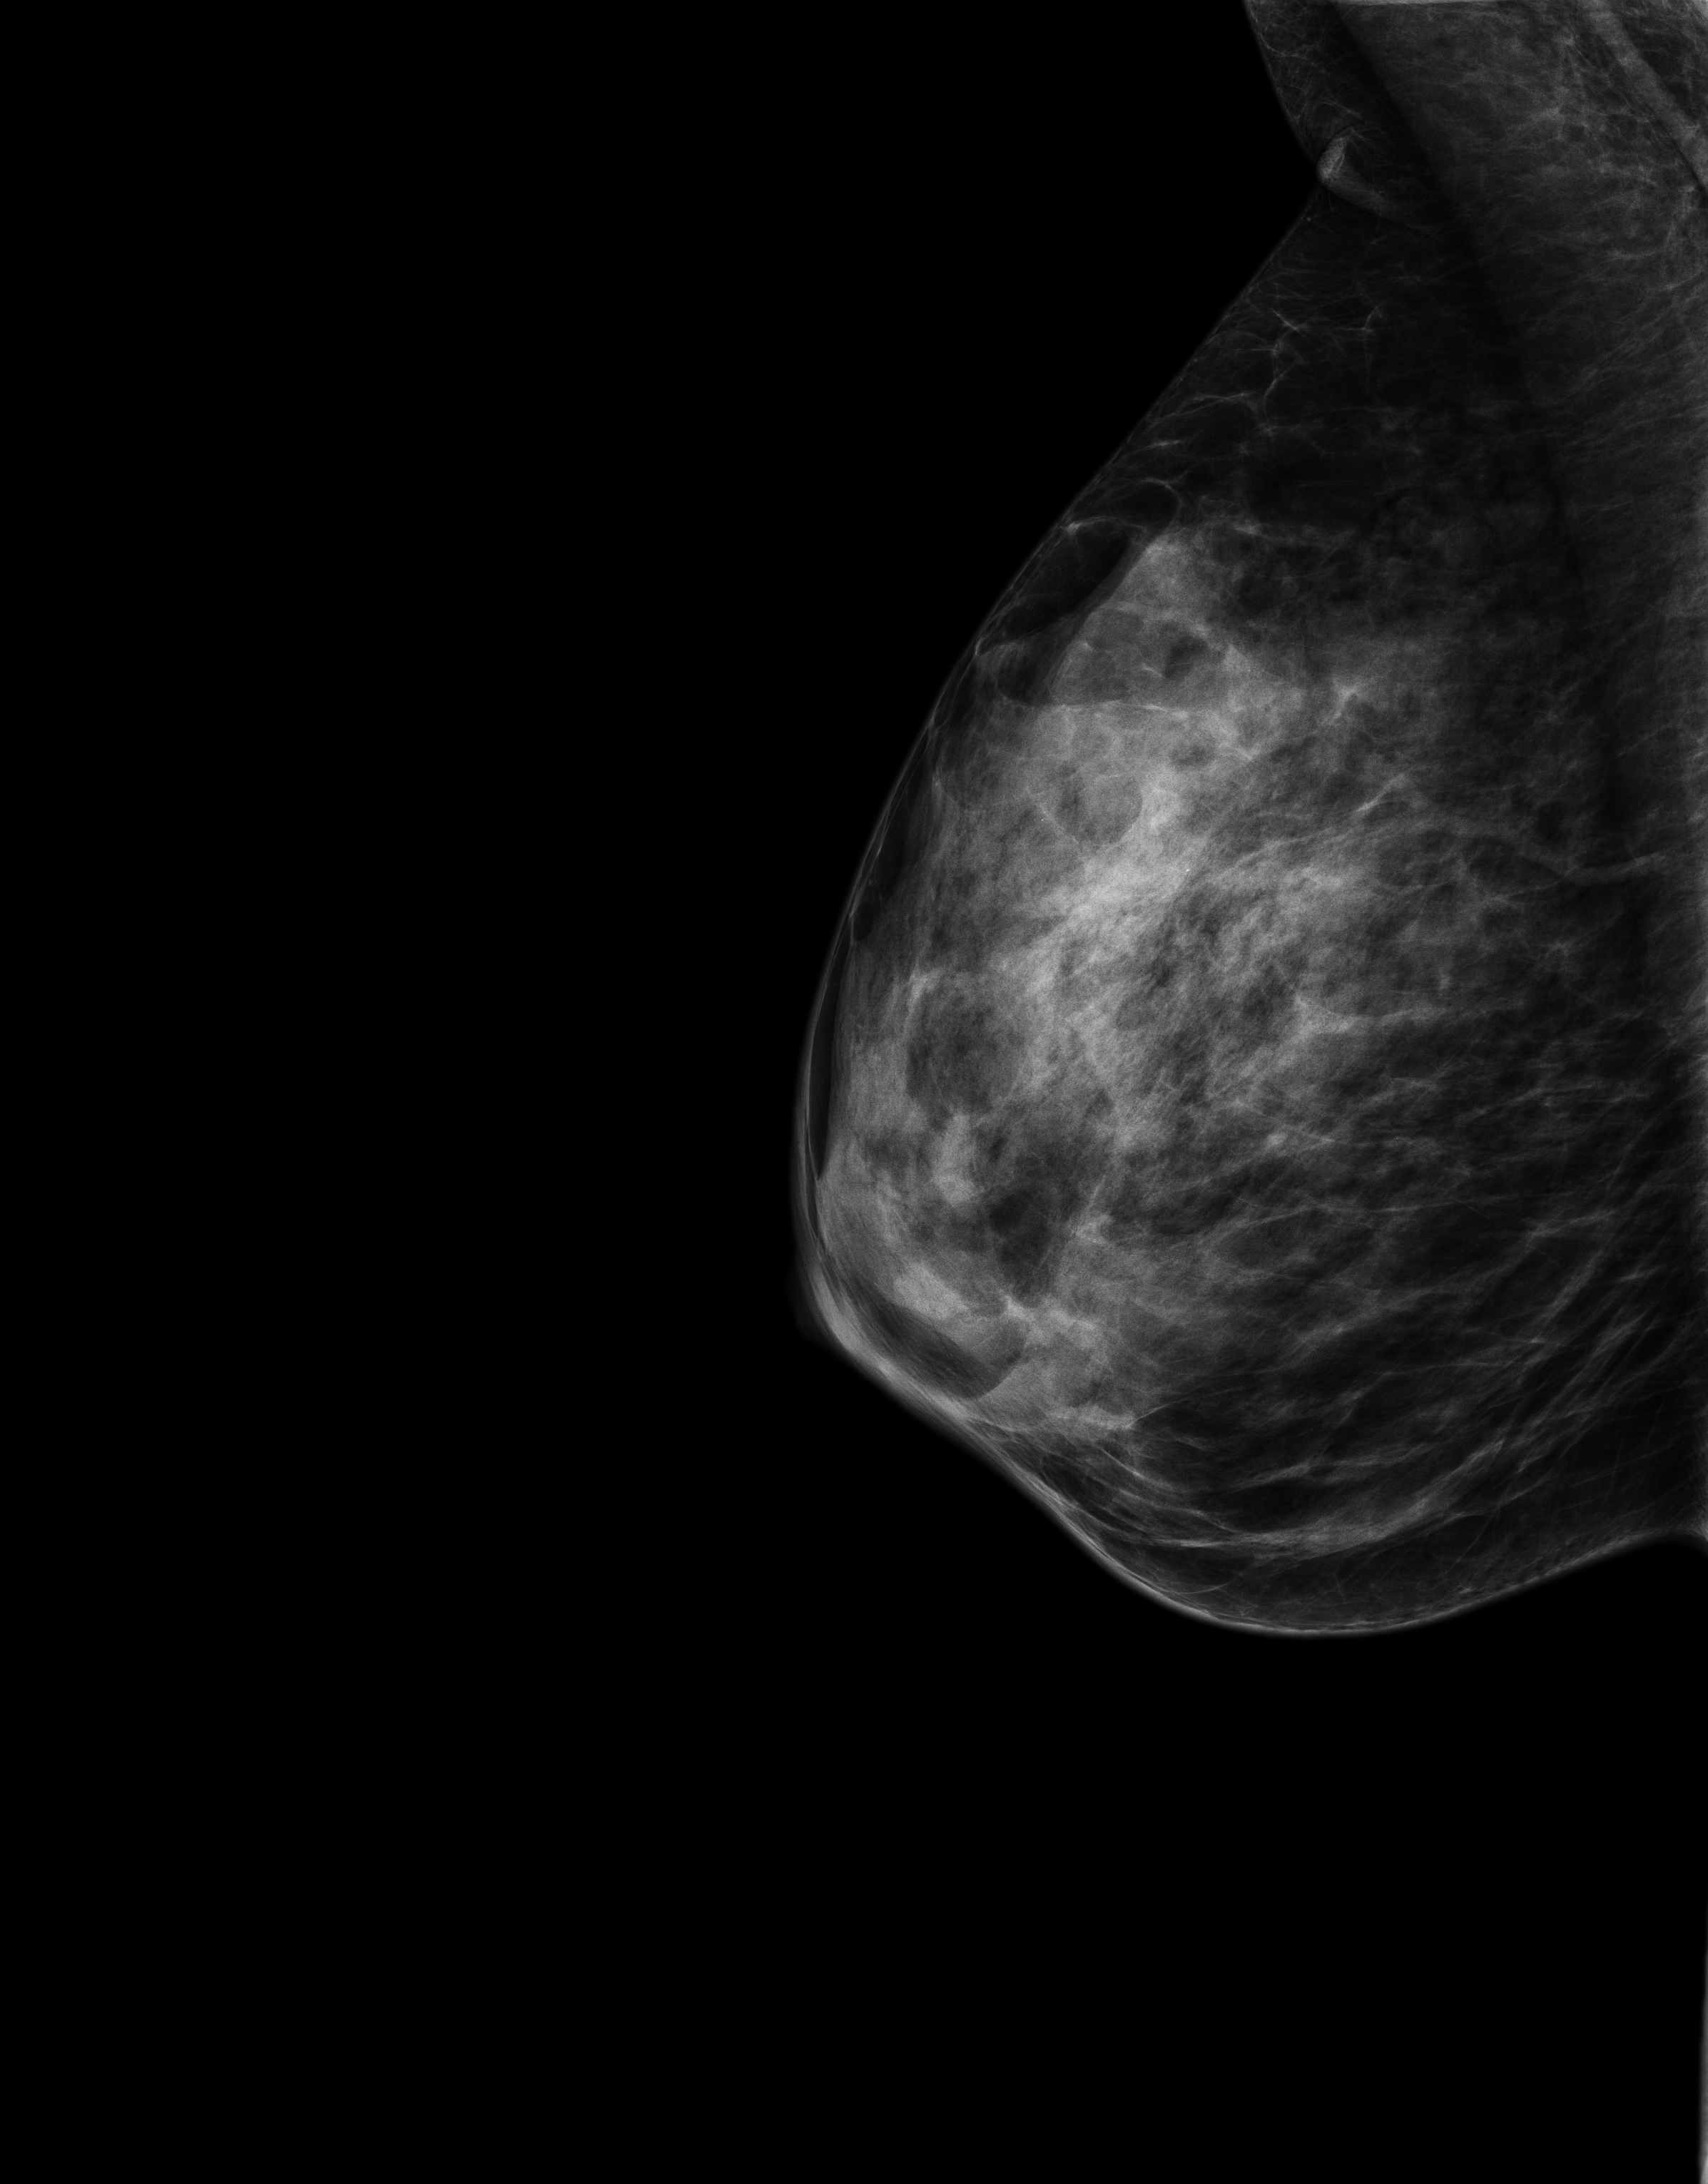
Annual screening mammography examination, system: Senographe Essential ADS_56.21.3. Patient aged 48 years (female).
Image type: full-field digital mammogram. Breast: right. Projection: mediolateral oblique (MLO) view.